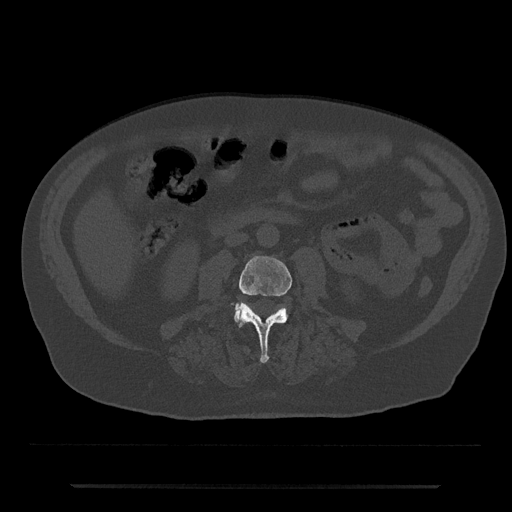
CT including the spine, one axial slice. Bone window (W 1800 / L 400 HU). 512 × 512 image matrix, field of view 434 × 434 mm. Patient: male, 80 years. From the clinical record (not read from this slice): primary cancer: prostate; vertebrae with lytic lesions (as recorded): L1, T11.
Annotated regions visible in this slice (semi-automatic segmentation, software-assisted and operator-edited):
- L3 vertebra: box from (x=233, y=256) to (x=292, y=363) px
- L4 vertebra: (x=234, y=306)–(x=287, y=322)